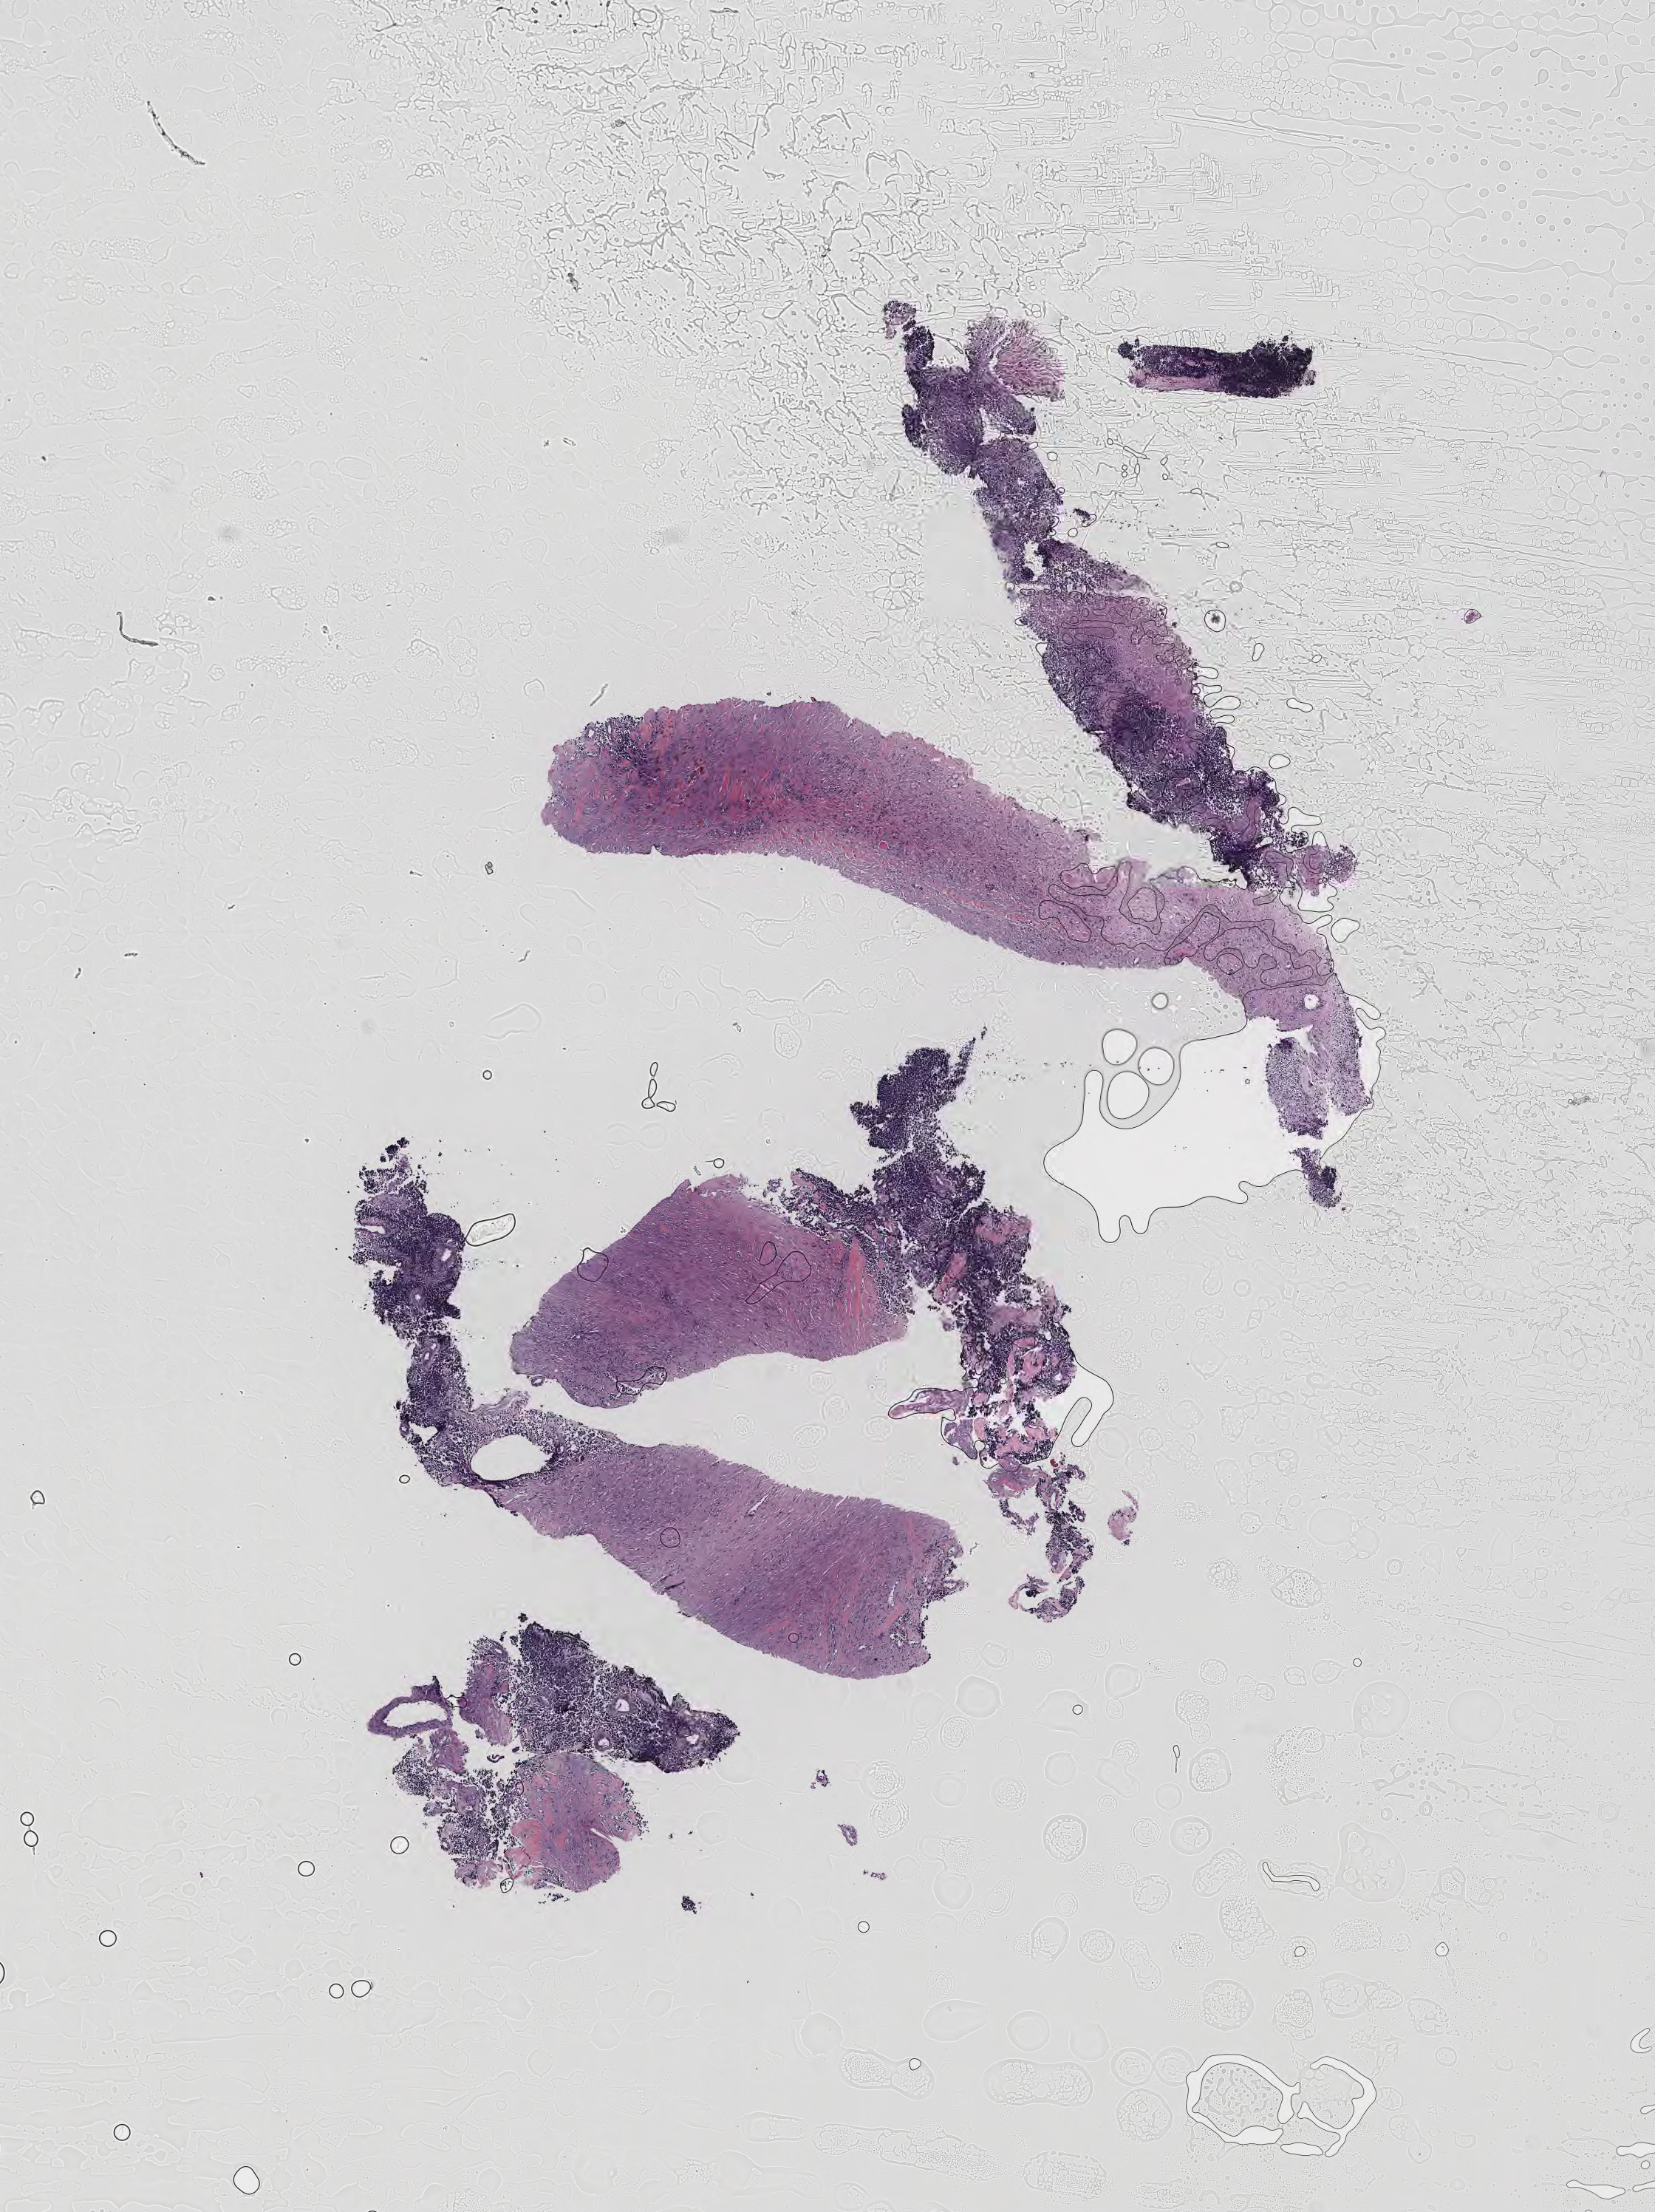
H&E whole-slide image of tumor tissue from the thorax, whole scanned area (about 9.1 x 12.1 mm) shown as a low-resolution overview. Formalin-fixed paraffin-embedded section. Patient: female, age 196 months (16 years 4 months).
- diagnosis: Rhabdomyosarcoma, NOS